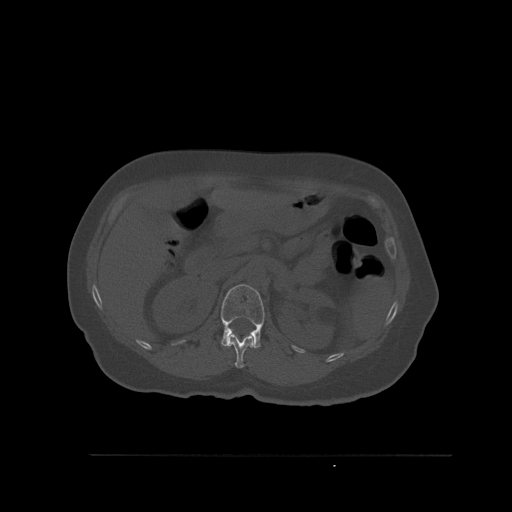
CT including the spine, one axial slice. Slice 273 of 527 in the series (ordered by position). Bone window (W 1800 / L 400 HU). 512 × 512 image matrix, field of view 470 × 470 mm. Female patient, age 73 years. Case-level facts recorded for this patient, not image findings: primary cancer: breast.
Structures marked on this image (semi-automatic segmentation, software-assisted and operator-edited):
- L1 vertebra: bounding box (x1, y1, x2, y2) in pixels: (220, 284, 265, 349)
- T12 vertebra: (227, 333, 254, 368)